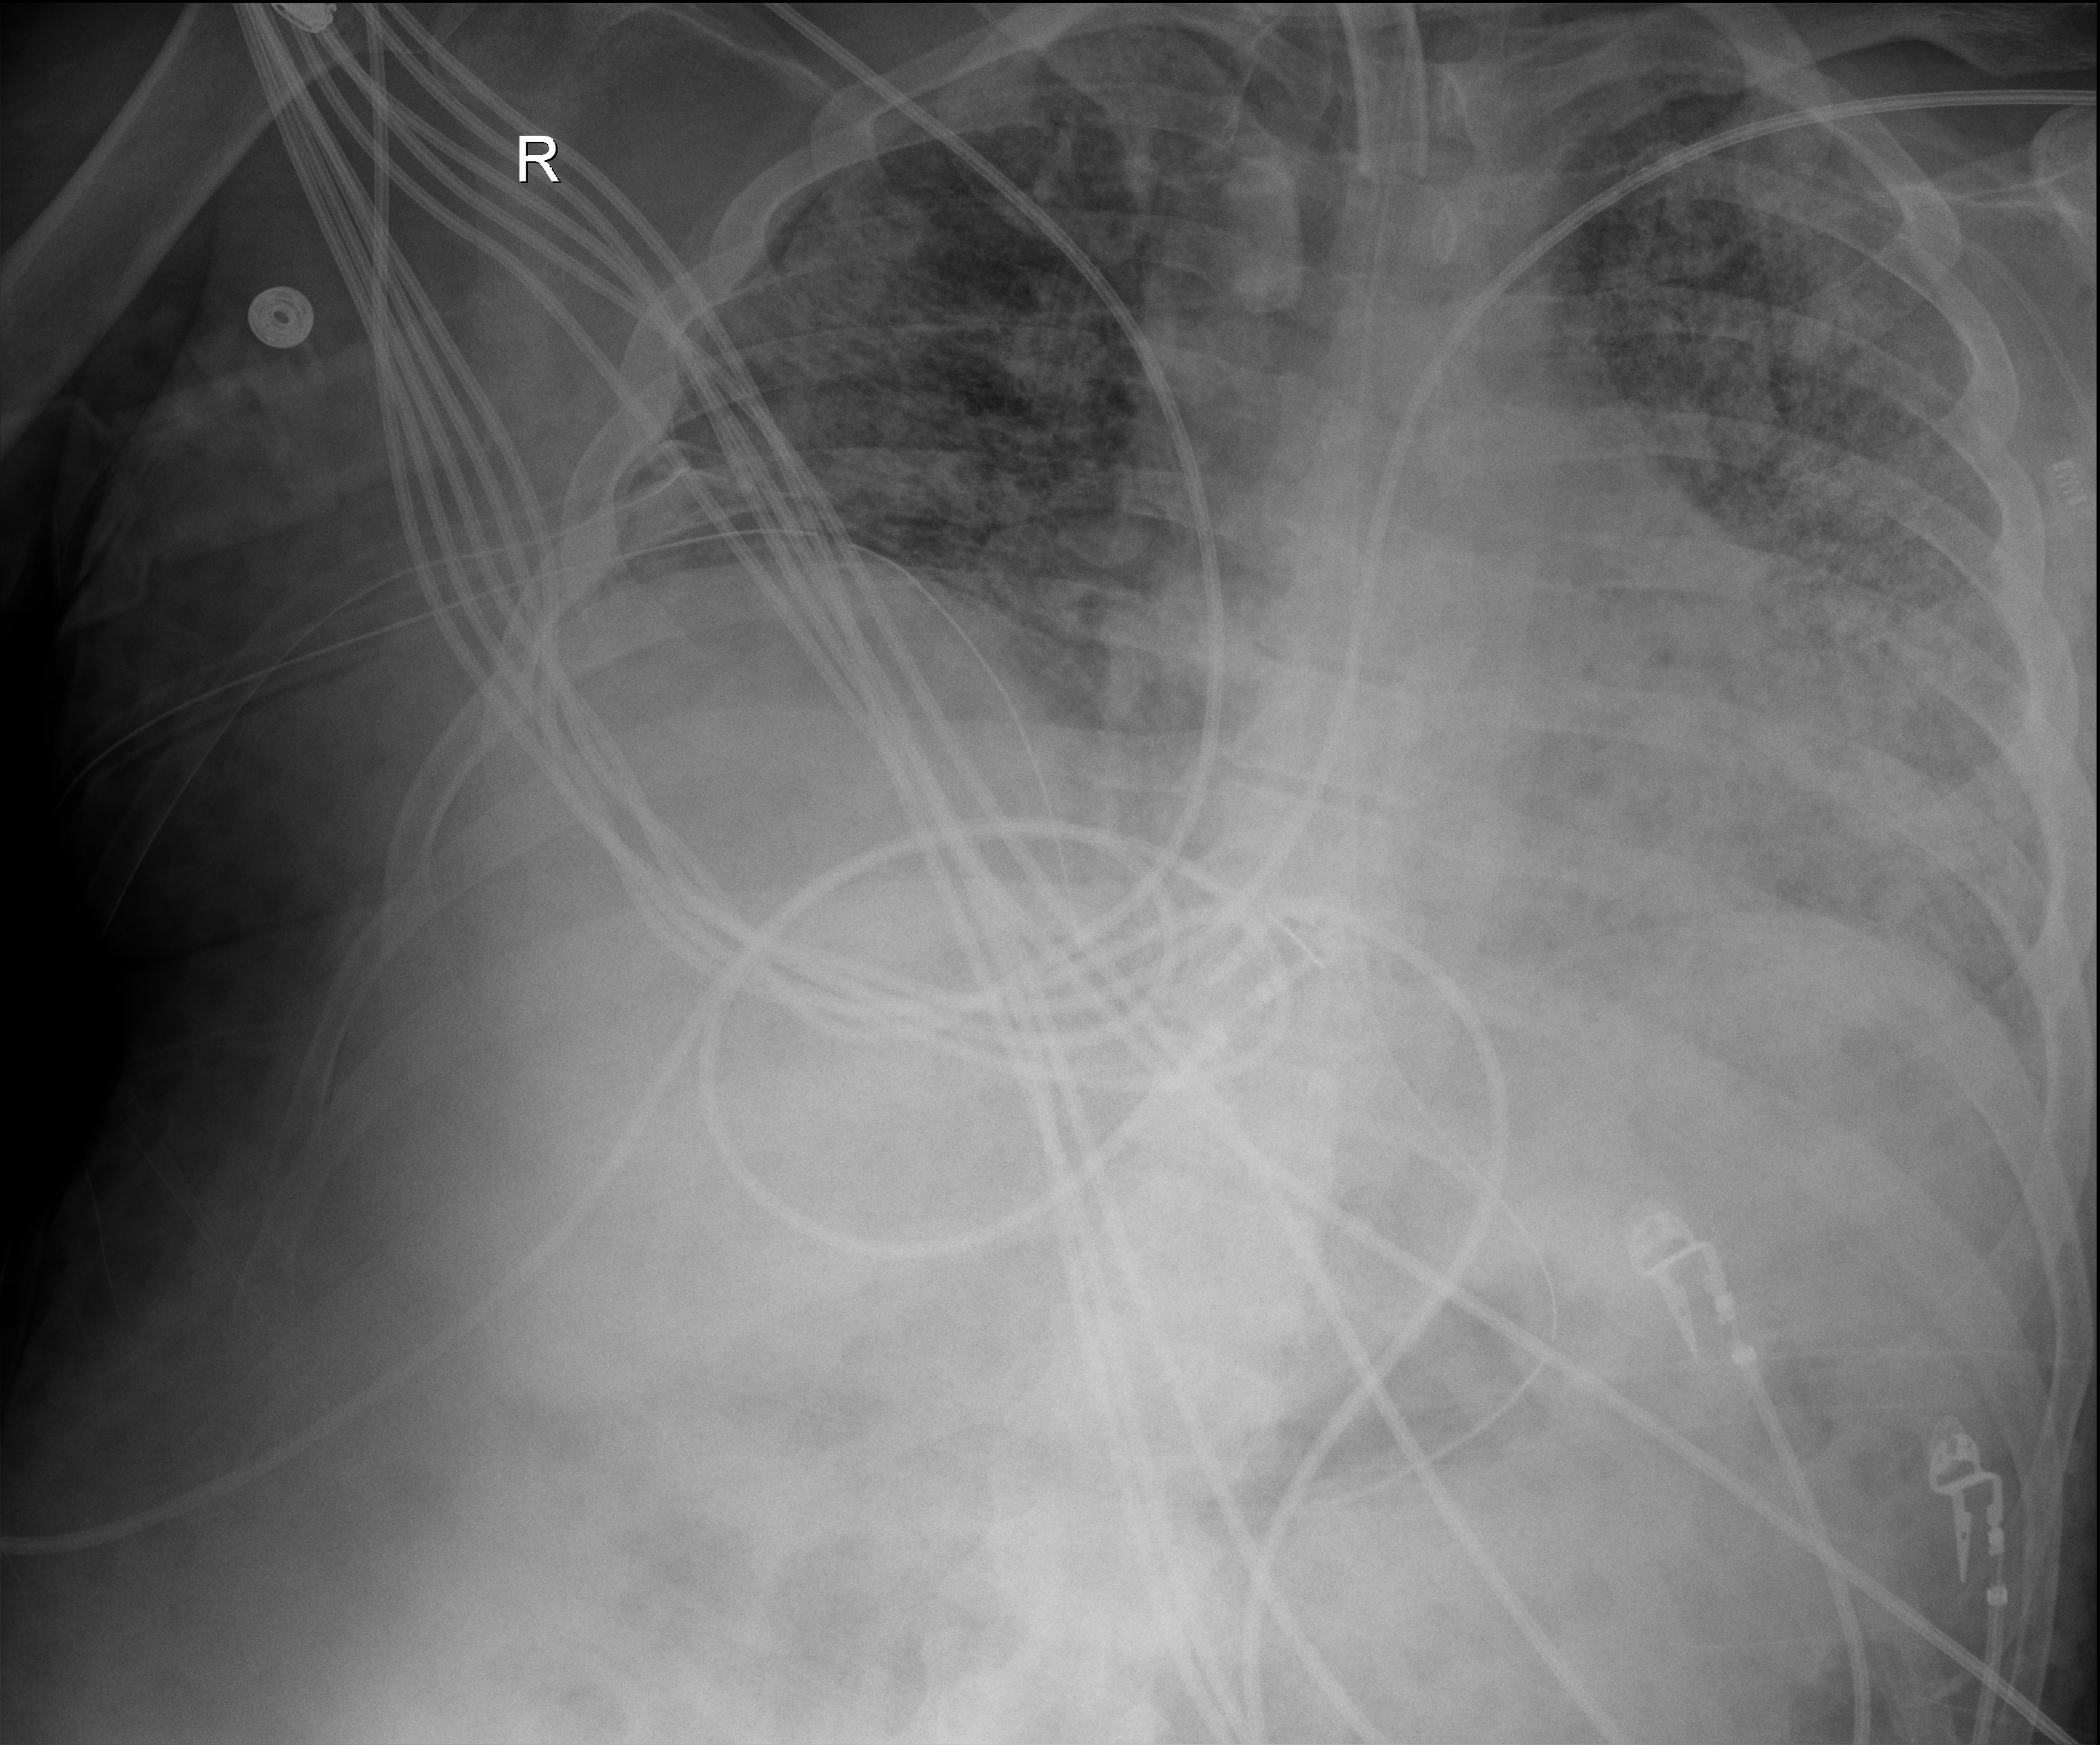
Chest radiograph (digital radiography), anteroposterior (AP) projection. Male patient hospitalised with COVID-19, age 18–59 years.
Hospital-stay facts (about this admission, not read from this image; timing relative to this image not recorded):
- smoking status (admission record): never